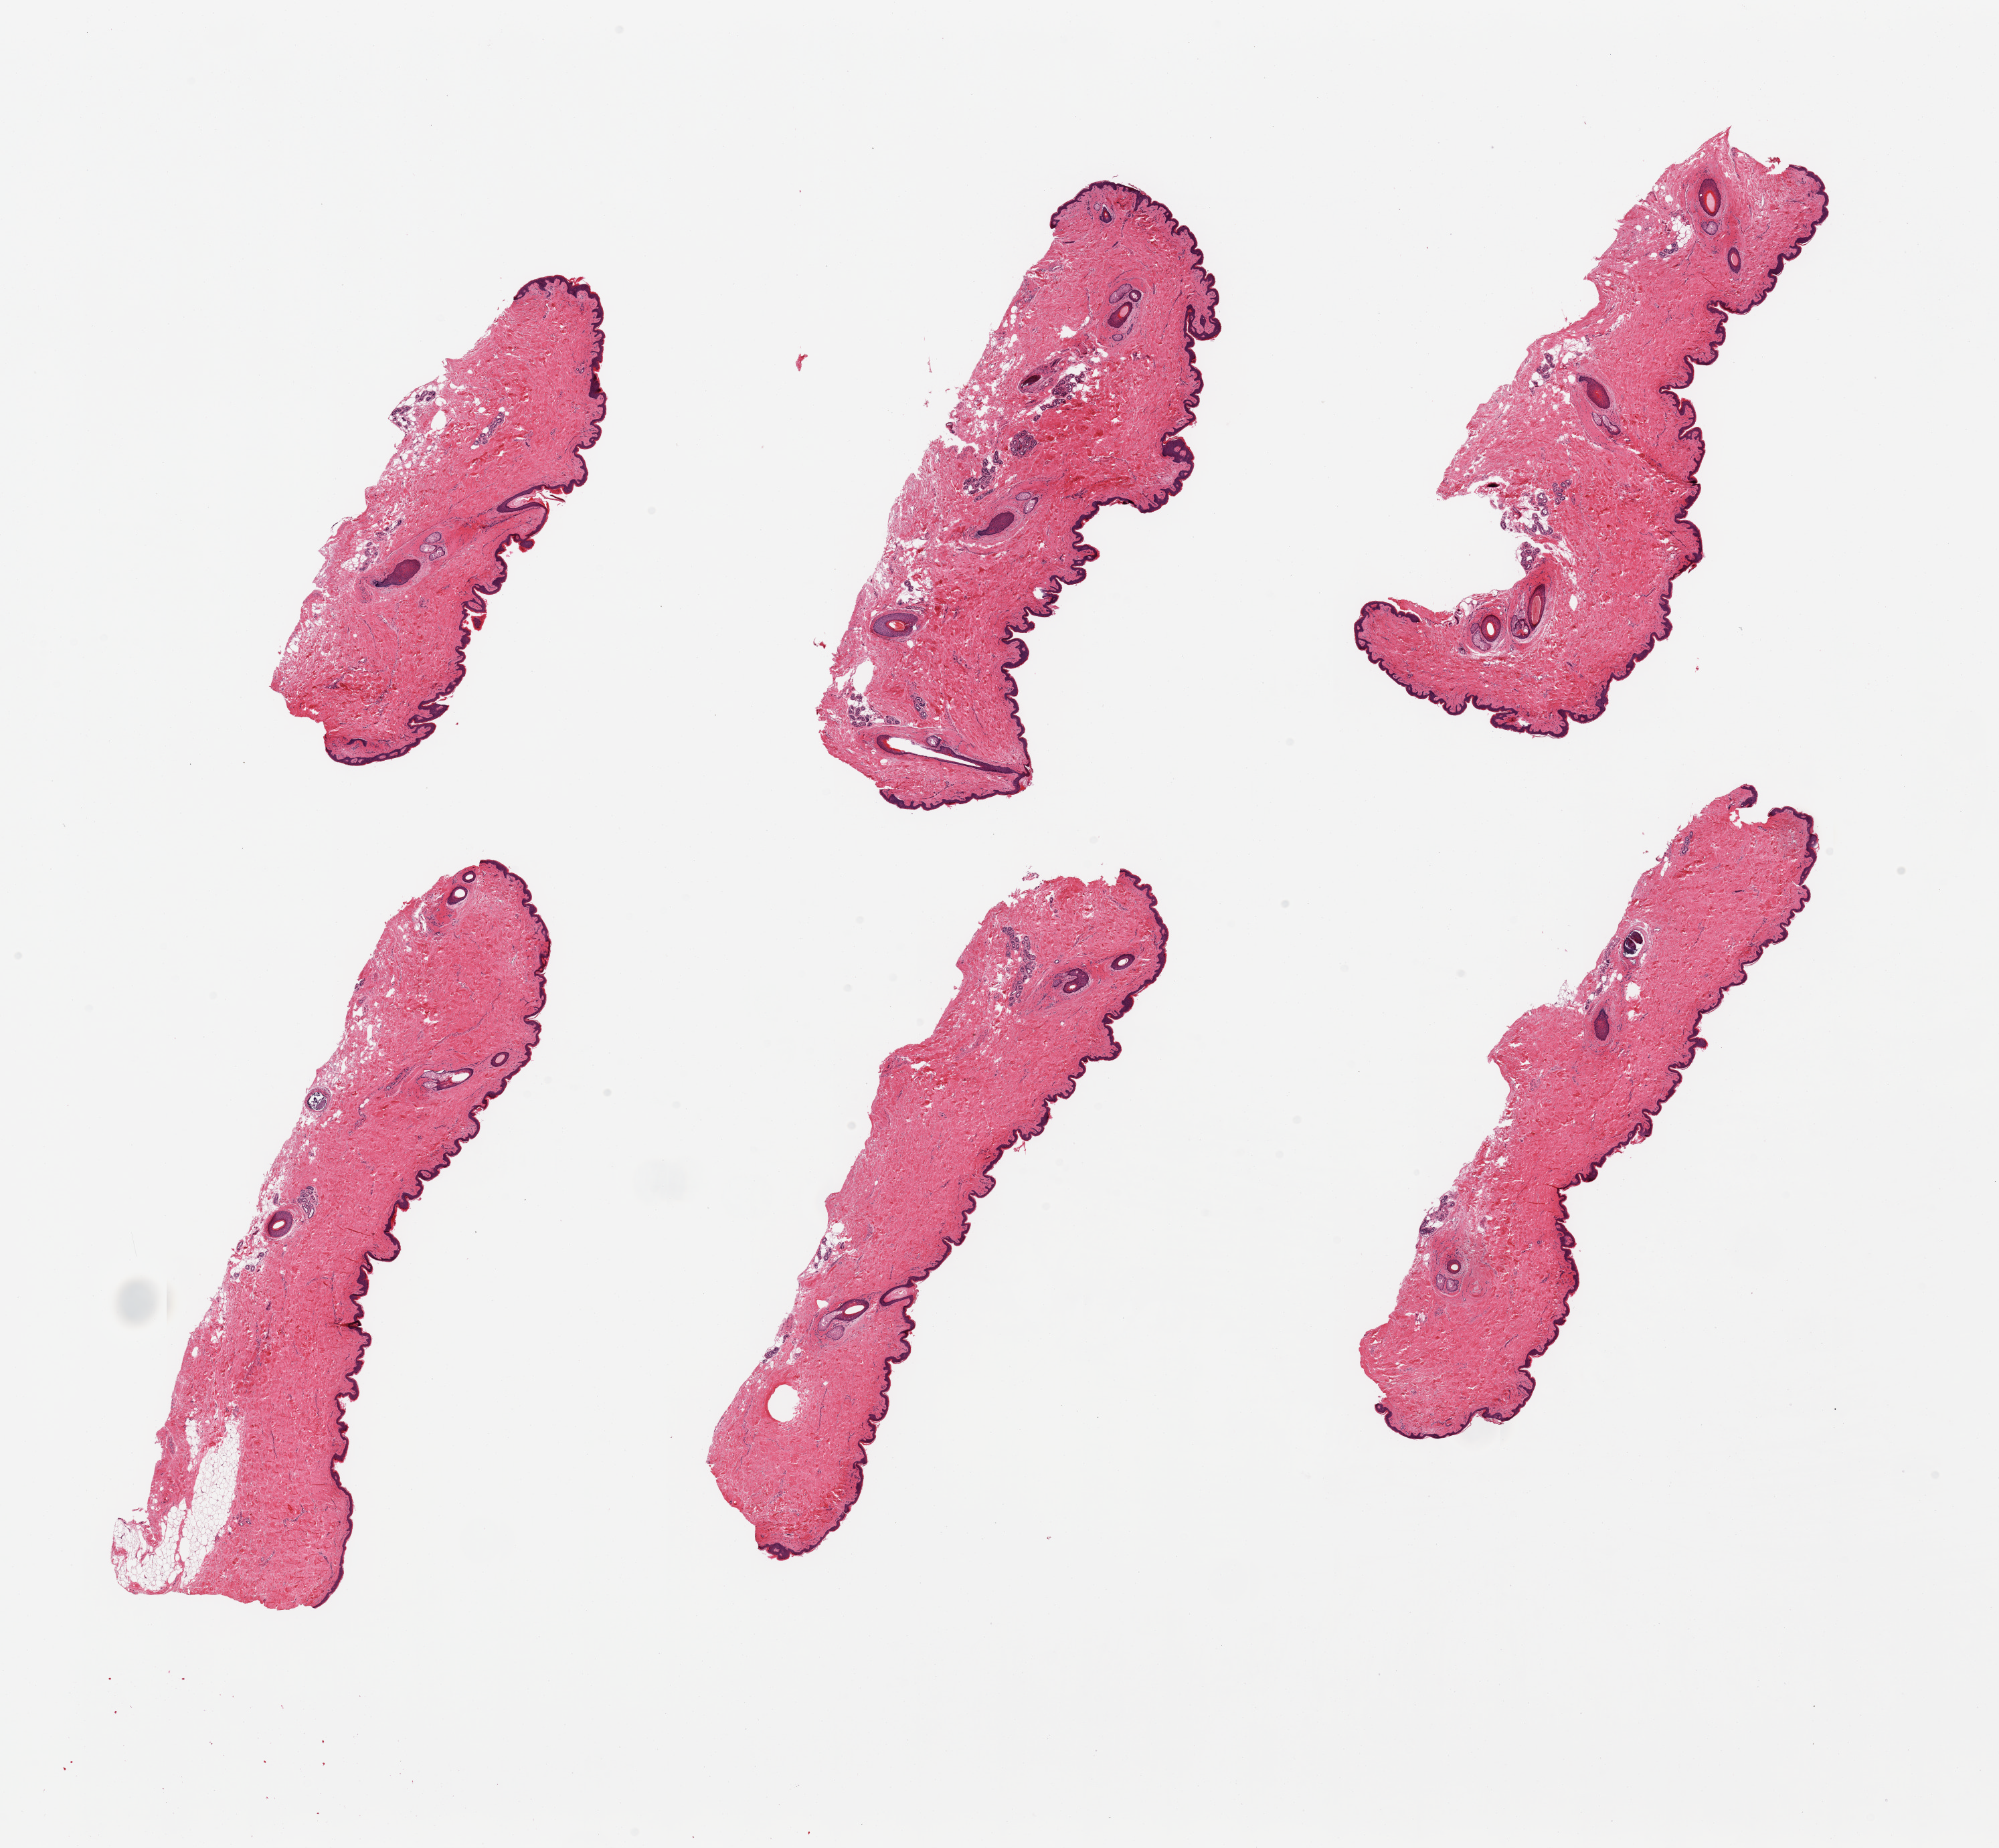
Whole-slide image, haematoxylin and eosin stain, a low-resolution overview of the entire scanned area, about 23.6 x 21.8 mm (slide scanned at 20x), PAXgene-fixed paraffin-embedded (PFPE) section, target tissue: skin of suprapubic region, donor tissue sample. Male donor.
Review note (as recorded): 6 pieces; hair bearing skin with minimal internal and external fat; squamous epithelium up to ~0.36um.